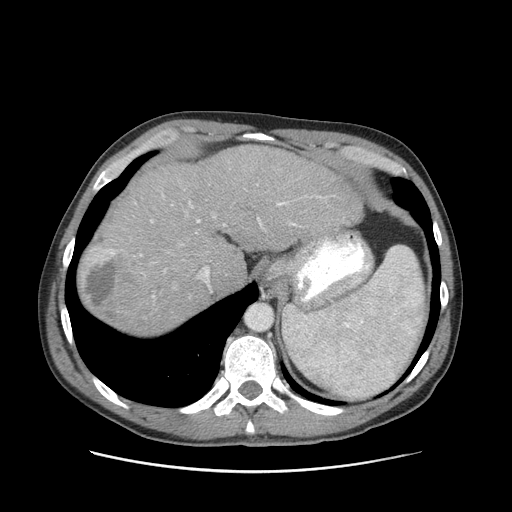
Contrast-enhanced abdominal CT (liver protocol), one axial slice. Slice 76 of 93 in the series (ordered by position). Reconstruction kernel STANDARD. Soft-tissue window (W 400 / L 40 HU). 2.5 mm slice thickness. 512 × 512 image matrix, field of view 380 × 380 mm. From the clinical record (not read from this slice): diagnosis: hepatocellular carcinoma (patient treated with transarterial chemoembolisation; whether this scan precedes or follows treatment is not stated here); TNM stage (as recorded): Stage-II; Child-Pugh class: A.
Structures marked on this image (semi-automatically segmented with operator editing):
- abdominal aorta: bounding box (x1, y1, x2, y2) in pixels: (246, 305, 272, 330)
- liver parenchyma outside the tumour (the mass and vessels are separate outlines, so this box may not span the whole liver): (78, 146, 362, 335)
- mass: (83, 246, 146, 322)
- liver vessels: (151, 202, 296, 297)